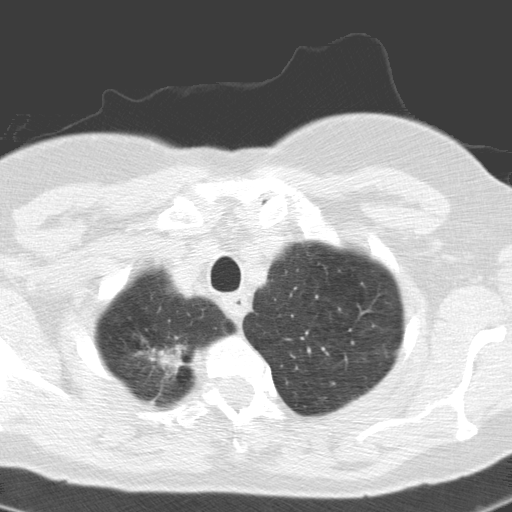
Axial slice from a low-dose chest CT screening exam, first (baseline) screen, lung window (W 1500 / L -600 HU), 3.2 mm slice thickness, slice 14 of 155 in the series. Female, age 60 years at enrolment. Current smoker at enrolment.
- Lesion marked by an expert reader, box from (x=119, y=330) to (x=197, y=402) px.
- Screening reader's record for this exam: no non-calcified nodule ≥4 mm recorded.
- Official screen result: negative screen, minor abnormalities not suspicious for lung cancer.
- Participant outcome: lung cancer diagnosed 391 days after this screen (after the second annual screen) — squamous cell carcinoma, keratinizing, NOS, right upper lobe, moderately differentiated (G2), stage IA (AJCC 6th edition), 20 mm at pathology.